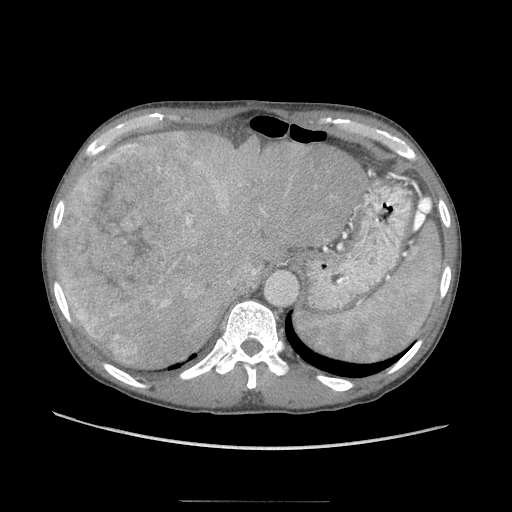
Contrast-enhanced abdominal CT (liver protocol), one axial slice; position 71 of 103 along the scan axis; 120 kVp; soft-tissue window (W 400 / L 40 HU); 2.5 mm slice thickness; 512 × 512 image matrix. From the clinical record (not read from this slice): diagnosis: hepatocellular carcinoma (patient treated with transarterial chemoembolisation; whether this scan precedes or follows treatment is not stated here); TNM stage (as recorded): Stage-IIIA.
Annotated regions visible in this slice (semi-automatically segmented with operator editing):
- liver parenchyma outside the tumour (the mass and vessels are separate outlines, so this box may not span the whole liver): bounding box <56,132,366,368> (left, top, right, bottom; pixels)
- mass: <59,142,190,362>
- liver vessels: <161,160,202,306>